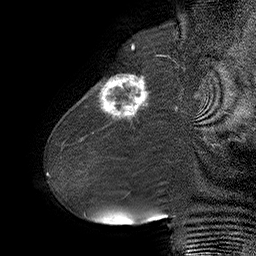
Breast MRI (dynamic contrast-enhanced), one sagittal slice; position 17 of 55 along the scan axis; dynamic contrast-enhanced series, time point 2 of 6 at this slice position (early post-contrast); 1.5 T; TE 4.5 ms, TR 32.4 ms; 256 × 256 image matrix, field of view 180 × 180 mm. Female patient. From the clinical record (not read from this slice): setting: breast cancer imaged before/during neoadjuvant chemotherapy; receptor status: HER2-positive.
Annotated regions visible in this slice (semi-automatically segmented with operator editing):
- analysis volume of interest (the breast-tissue region the enhancement analysis was run in; not a lesion): box from (x=80, y=64) to (x=163, y=134) px
- tumour enhancement mask (voxels above the 100 % enhancement threshold inside the analysis volume of interest): (x=99, y=75)–(x=148, y=122)